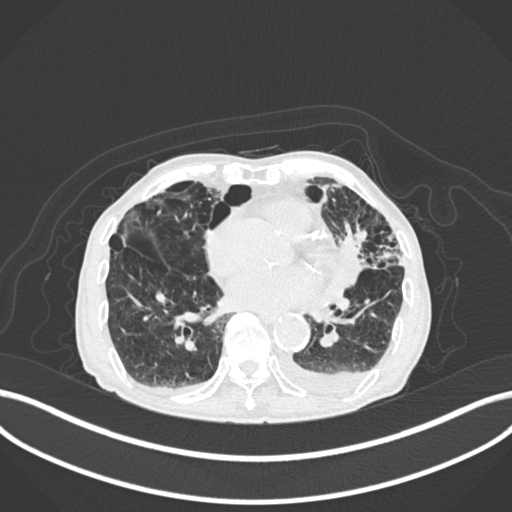
Chest CT, one axial slice; position 81 of 400 along the scan axis; reconstruction kernel B30f; 120 kVp; lung window (W 1500 / L -600 HU); 512 × 512 image matrix, field of view 400 × 400 mm. Male patient, age 90 years or older. From the clinical record (not read from this slice): clinical TNM (as recorded): T2b N1 M0.
Structures marked on this image (rectangle marked by the reading radiologist):
- lung tumour (recorded histology: squamous cell carcinoma): bounding box (x1, y1, x2, y2) in pixels: (331, 226, 368, 293)